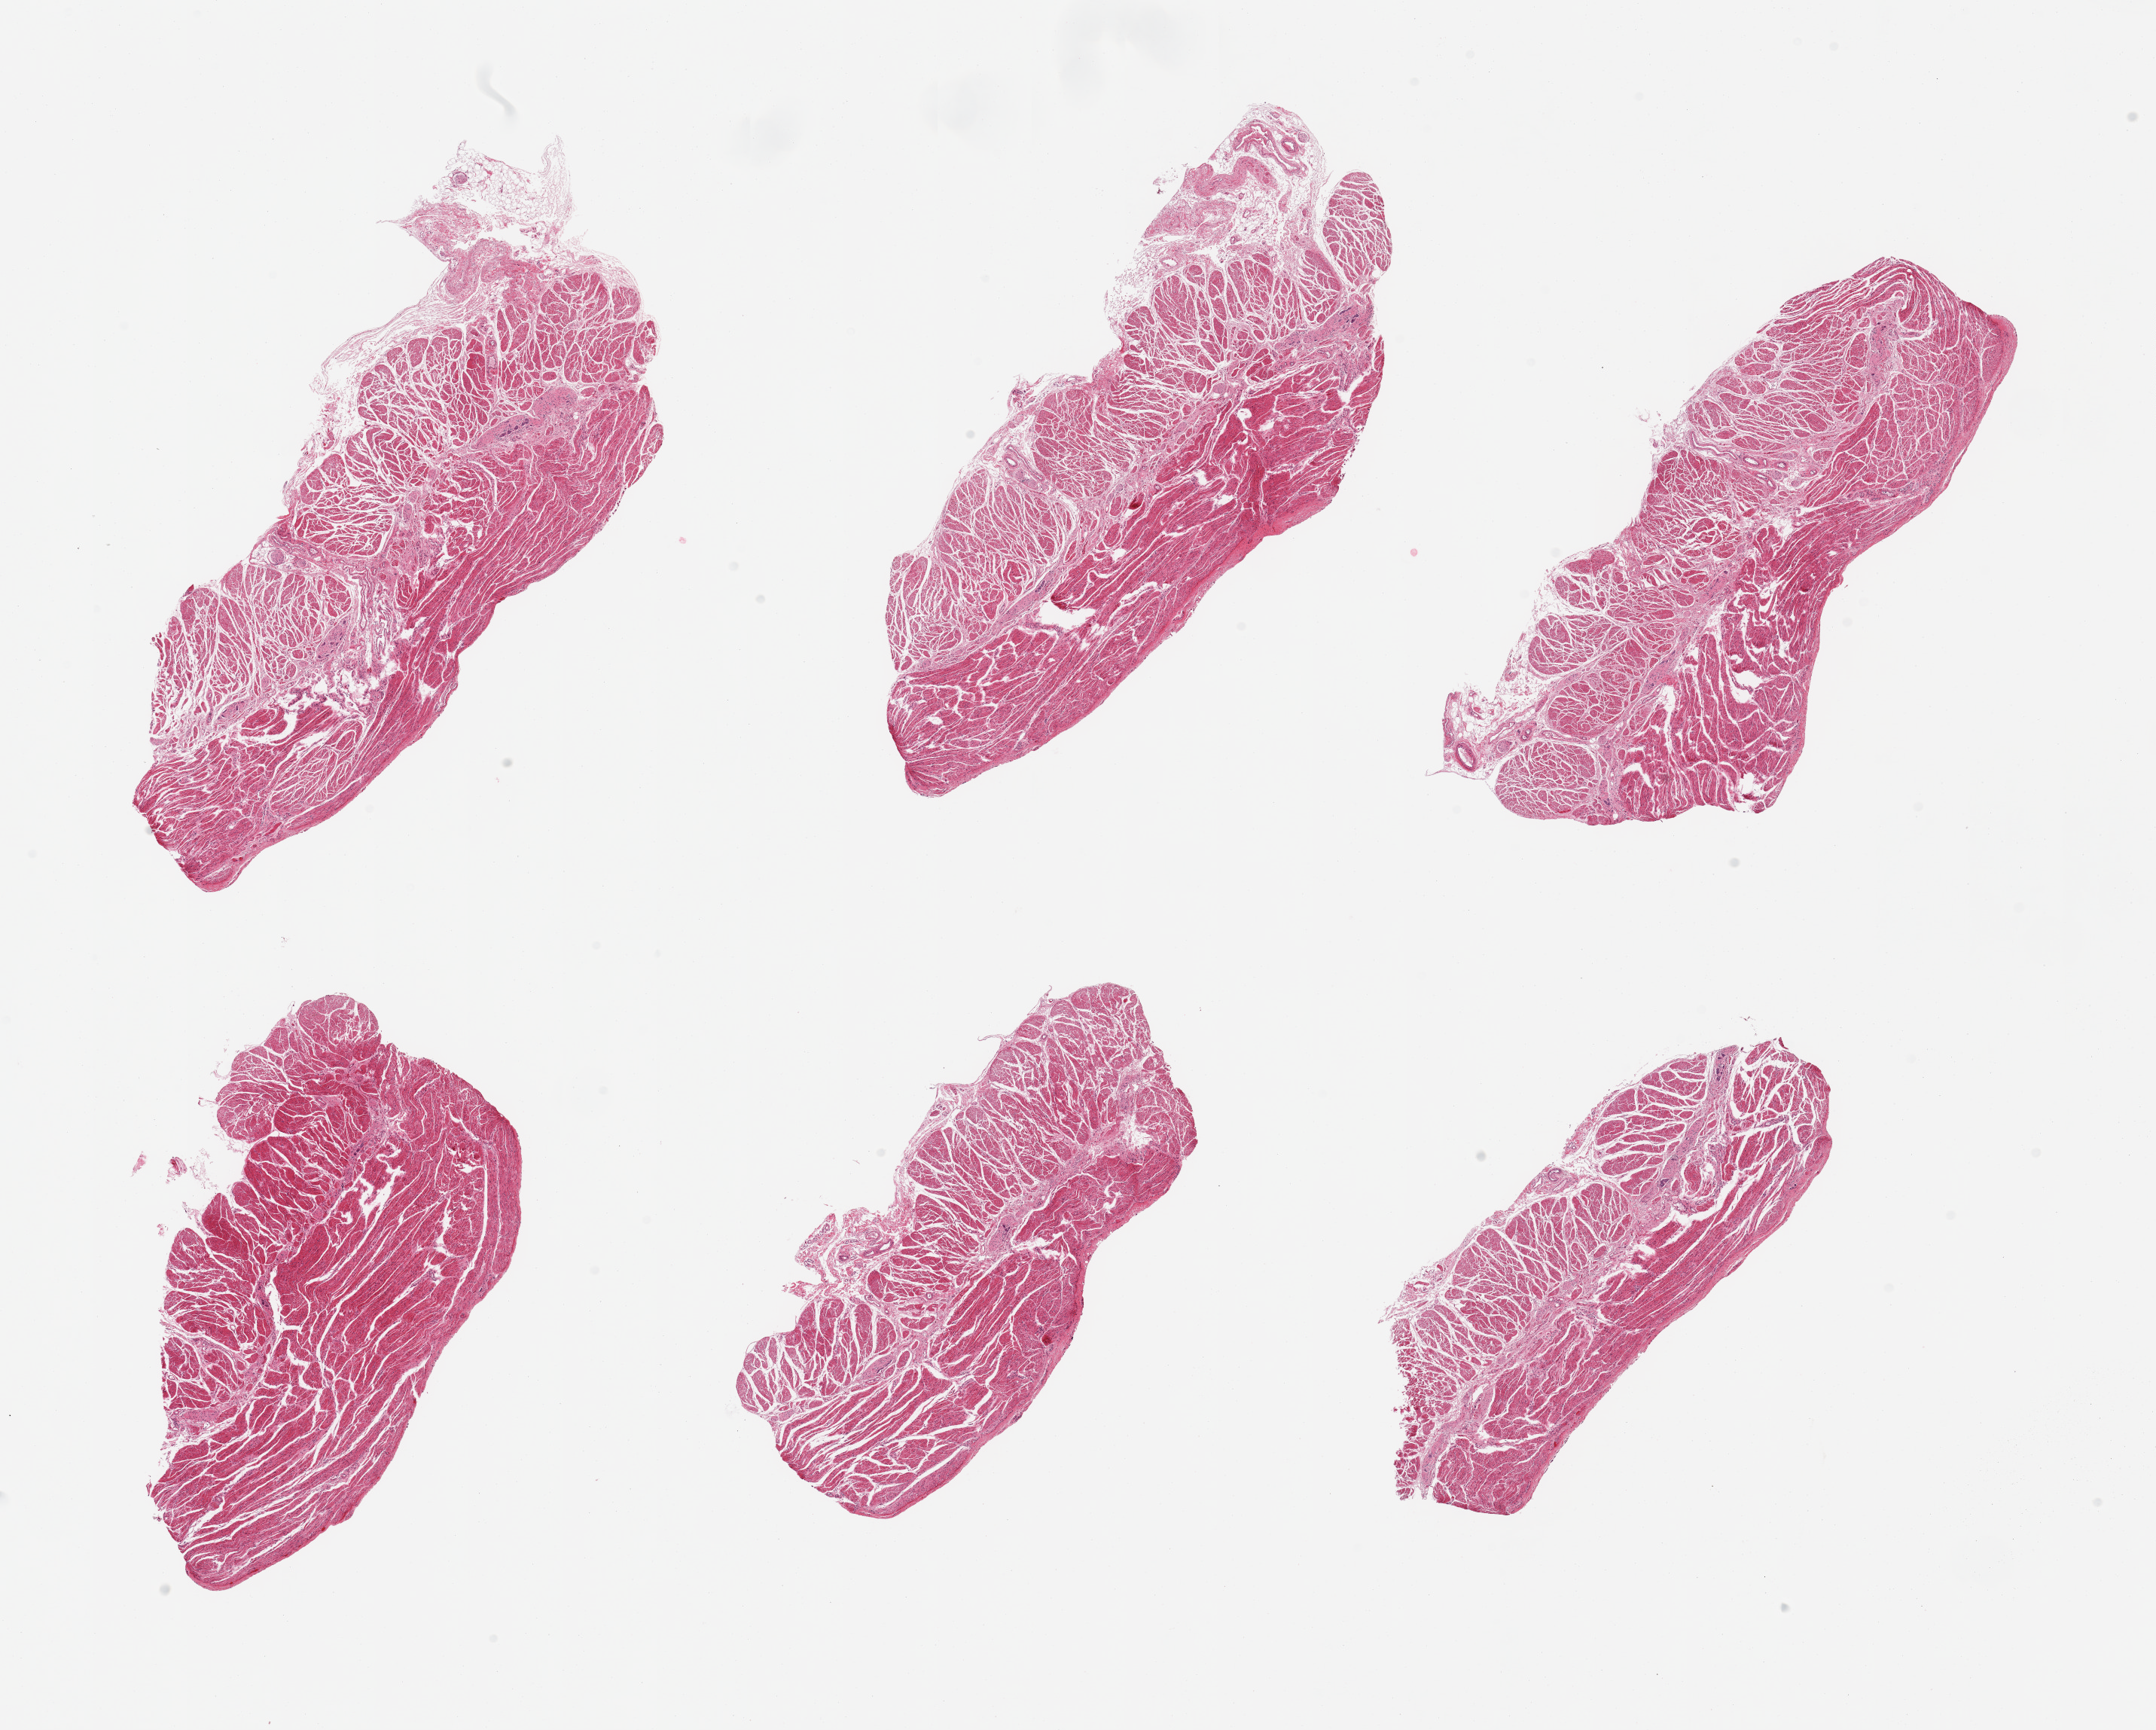
Digitized hematoxylin and eosin (H&E)-stained section — low-resolution overview of the scanned area, about 22.6 x 18.2 mm, PAXgene-fixed paraffin-embedded (PFPE) section, sampled site (target tissue): gastroesophageal junction, tissue donor sample. Donor: female.
Pathologist's review note for this sample: 6 pieces; confirmed target muscularis.